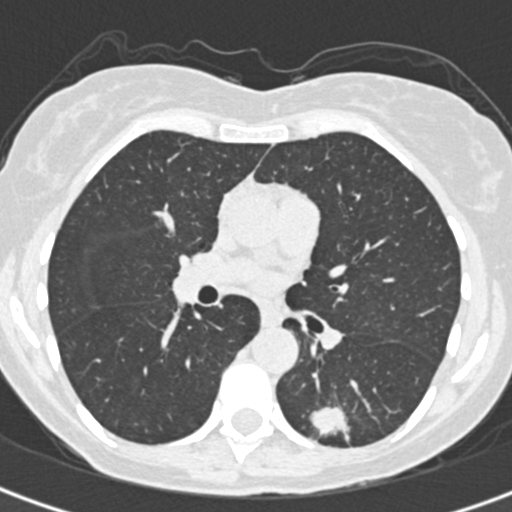
Low-dose screening chest CT, one axial slice. 120 kVp. Lung window (W 1500 / L -600 HU). 1 mm slice thickness. 512 × 512 image matrix, field of view 284 × 284 mm.
Annotated regions visible in this slice (manually delineated by an expert):
- lesion 1 (tumor, lower lobe of left lung): bounding box <311,407,348,435> (left, top, right, bottom; pixels)